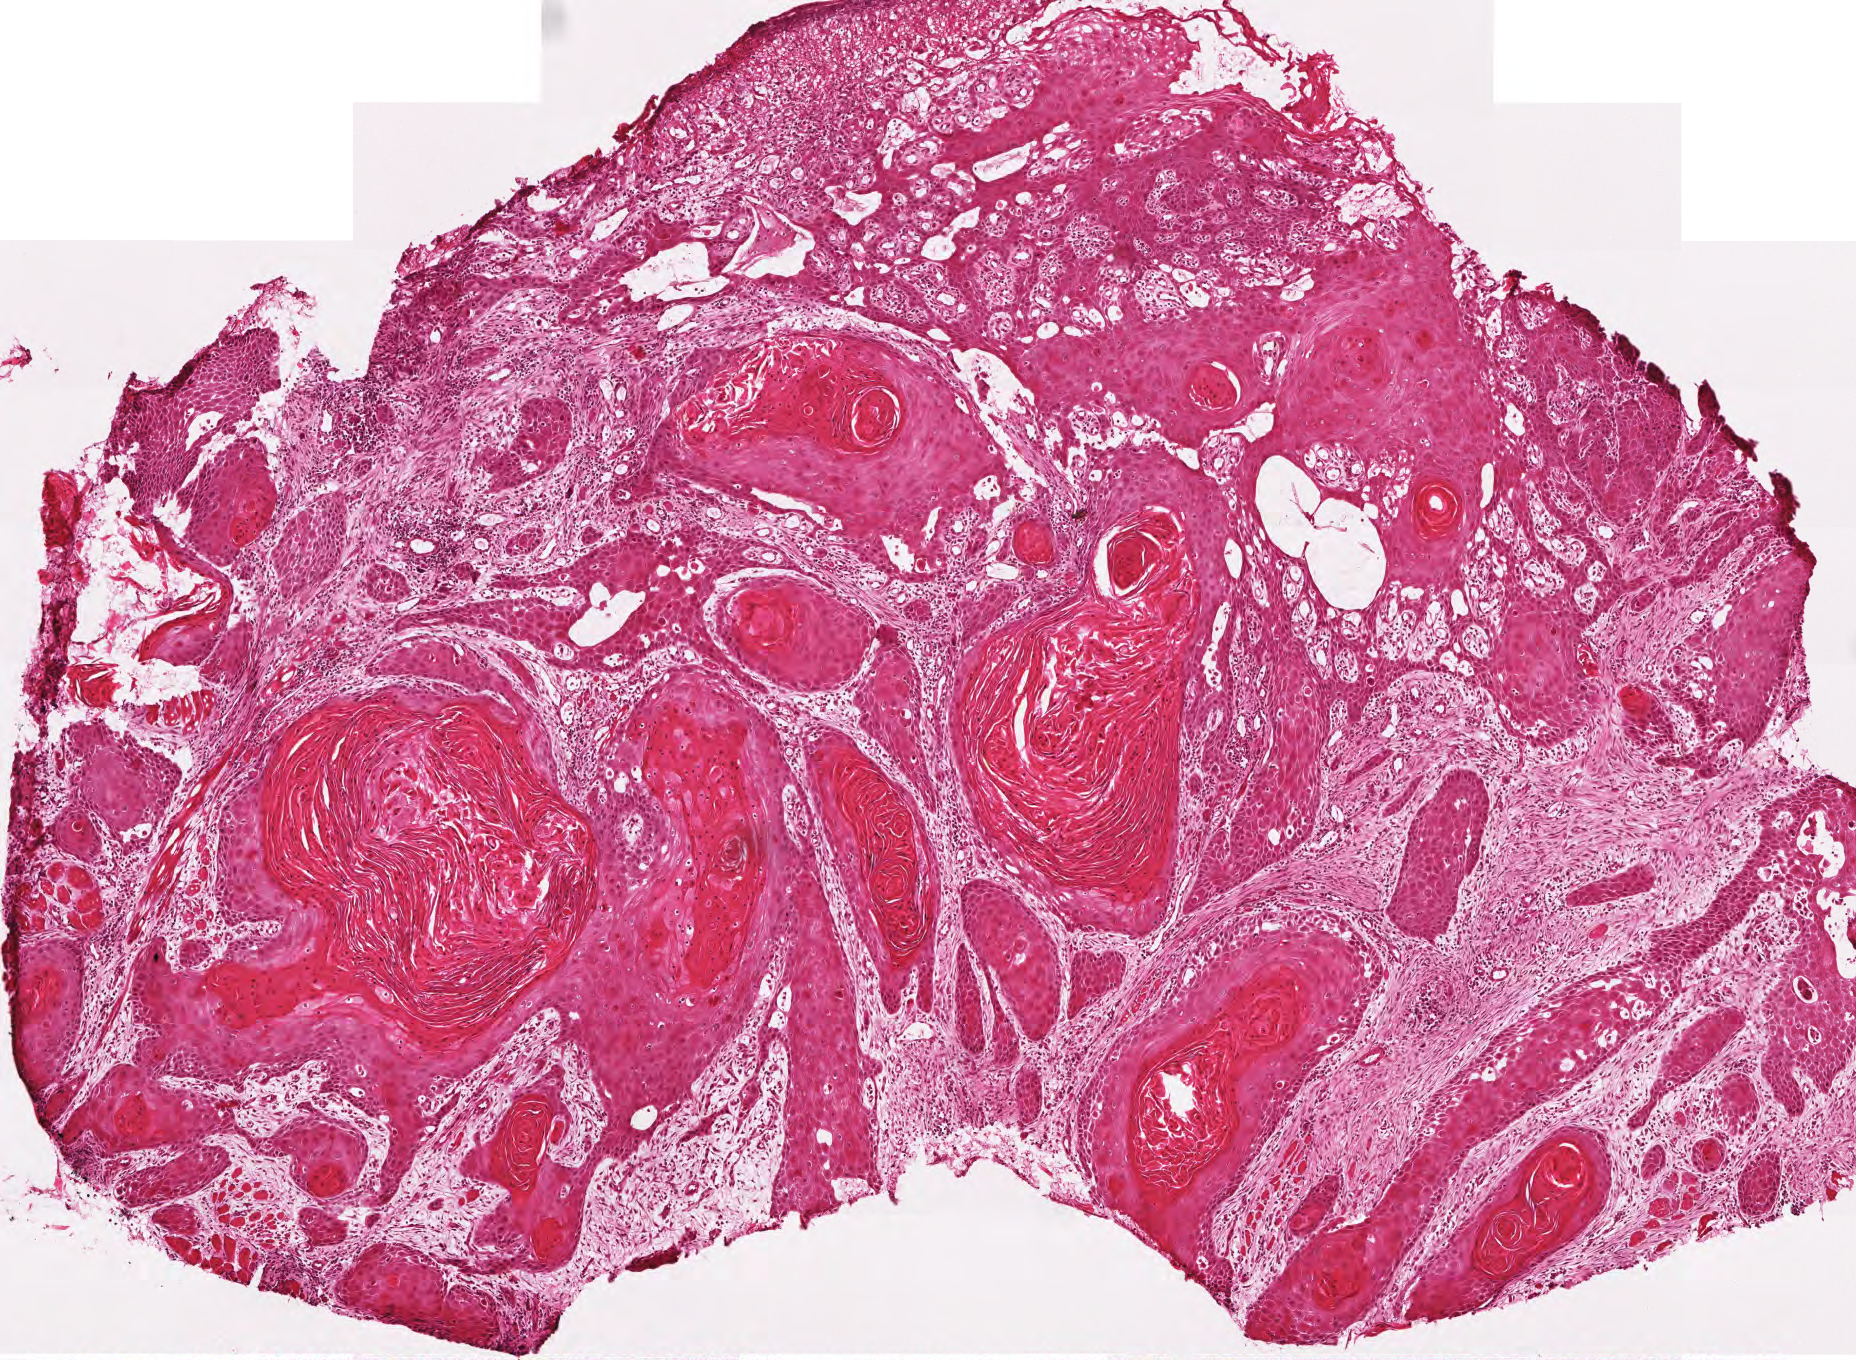
Whole-slide histology image, Hematoxylin and eosin (H&E) stained — low-resolution overview of the scanned area, about 3.7 x 2.7 mm, frozen section from the top of the tissue portion, sample: primary tumour, head and neck. Patient: male, age at initial diagnosis 45 years. Histologic grade: G1 (well differentiated). Pathologist review of this section (percent, as recorded): tumour cells 75%, tumour nuclei 60%, normal cells 0%, stromal cells 25%, necrosis 0%.
- AJCC pathologic stage: I
- pathologic diagnosis: Squamous cell carcinoma, NOS (tongue, NOS)
- laterality: left